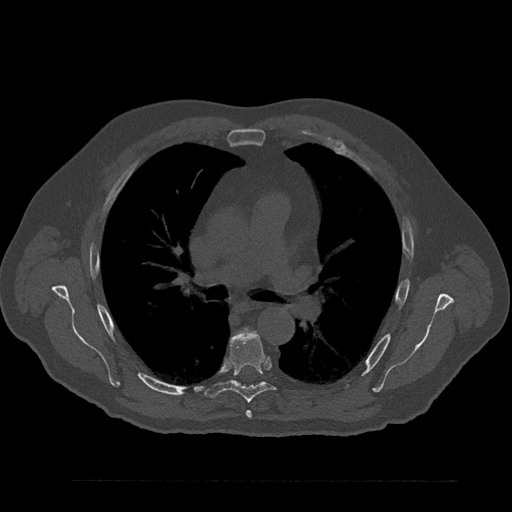
CT including the spine, one axial slice; position 560 of 797 along the scan axis; reconstruction kernel Br40s/3; bone window (W 1800 / L 400 HU); 0.5 mm slice thickness; 512 × 512 image matrix, field of view 430 × 430 mm. Patient: male, 61 years. From the clinical record (not read from this slice): primary cancer: prostate.
Annotated regions visible in this slice (semi-automatically segmented with operator editing):
- T5 vertebra: box from (x=246, y=410) to (x=252, y=419) px
- T6 vertebra: (x=205, y=331)–(x=276, y=403)